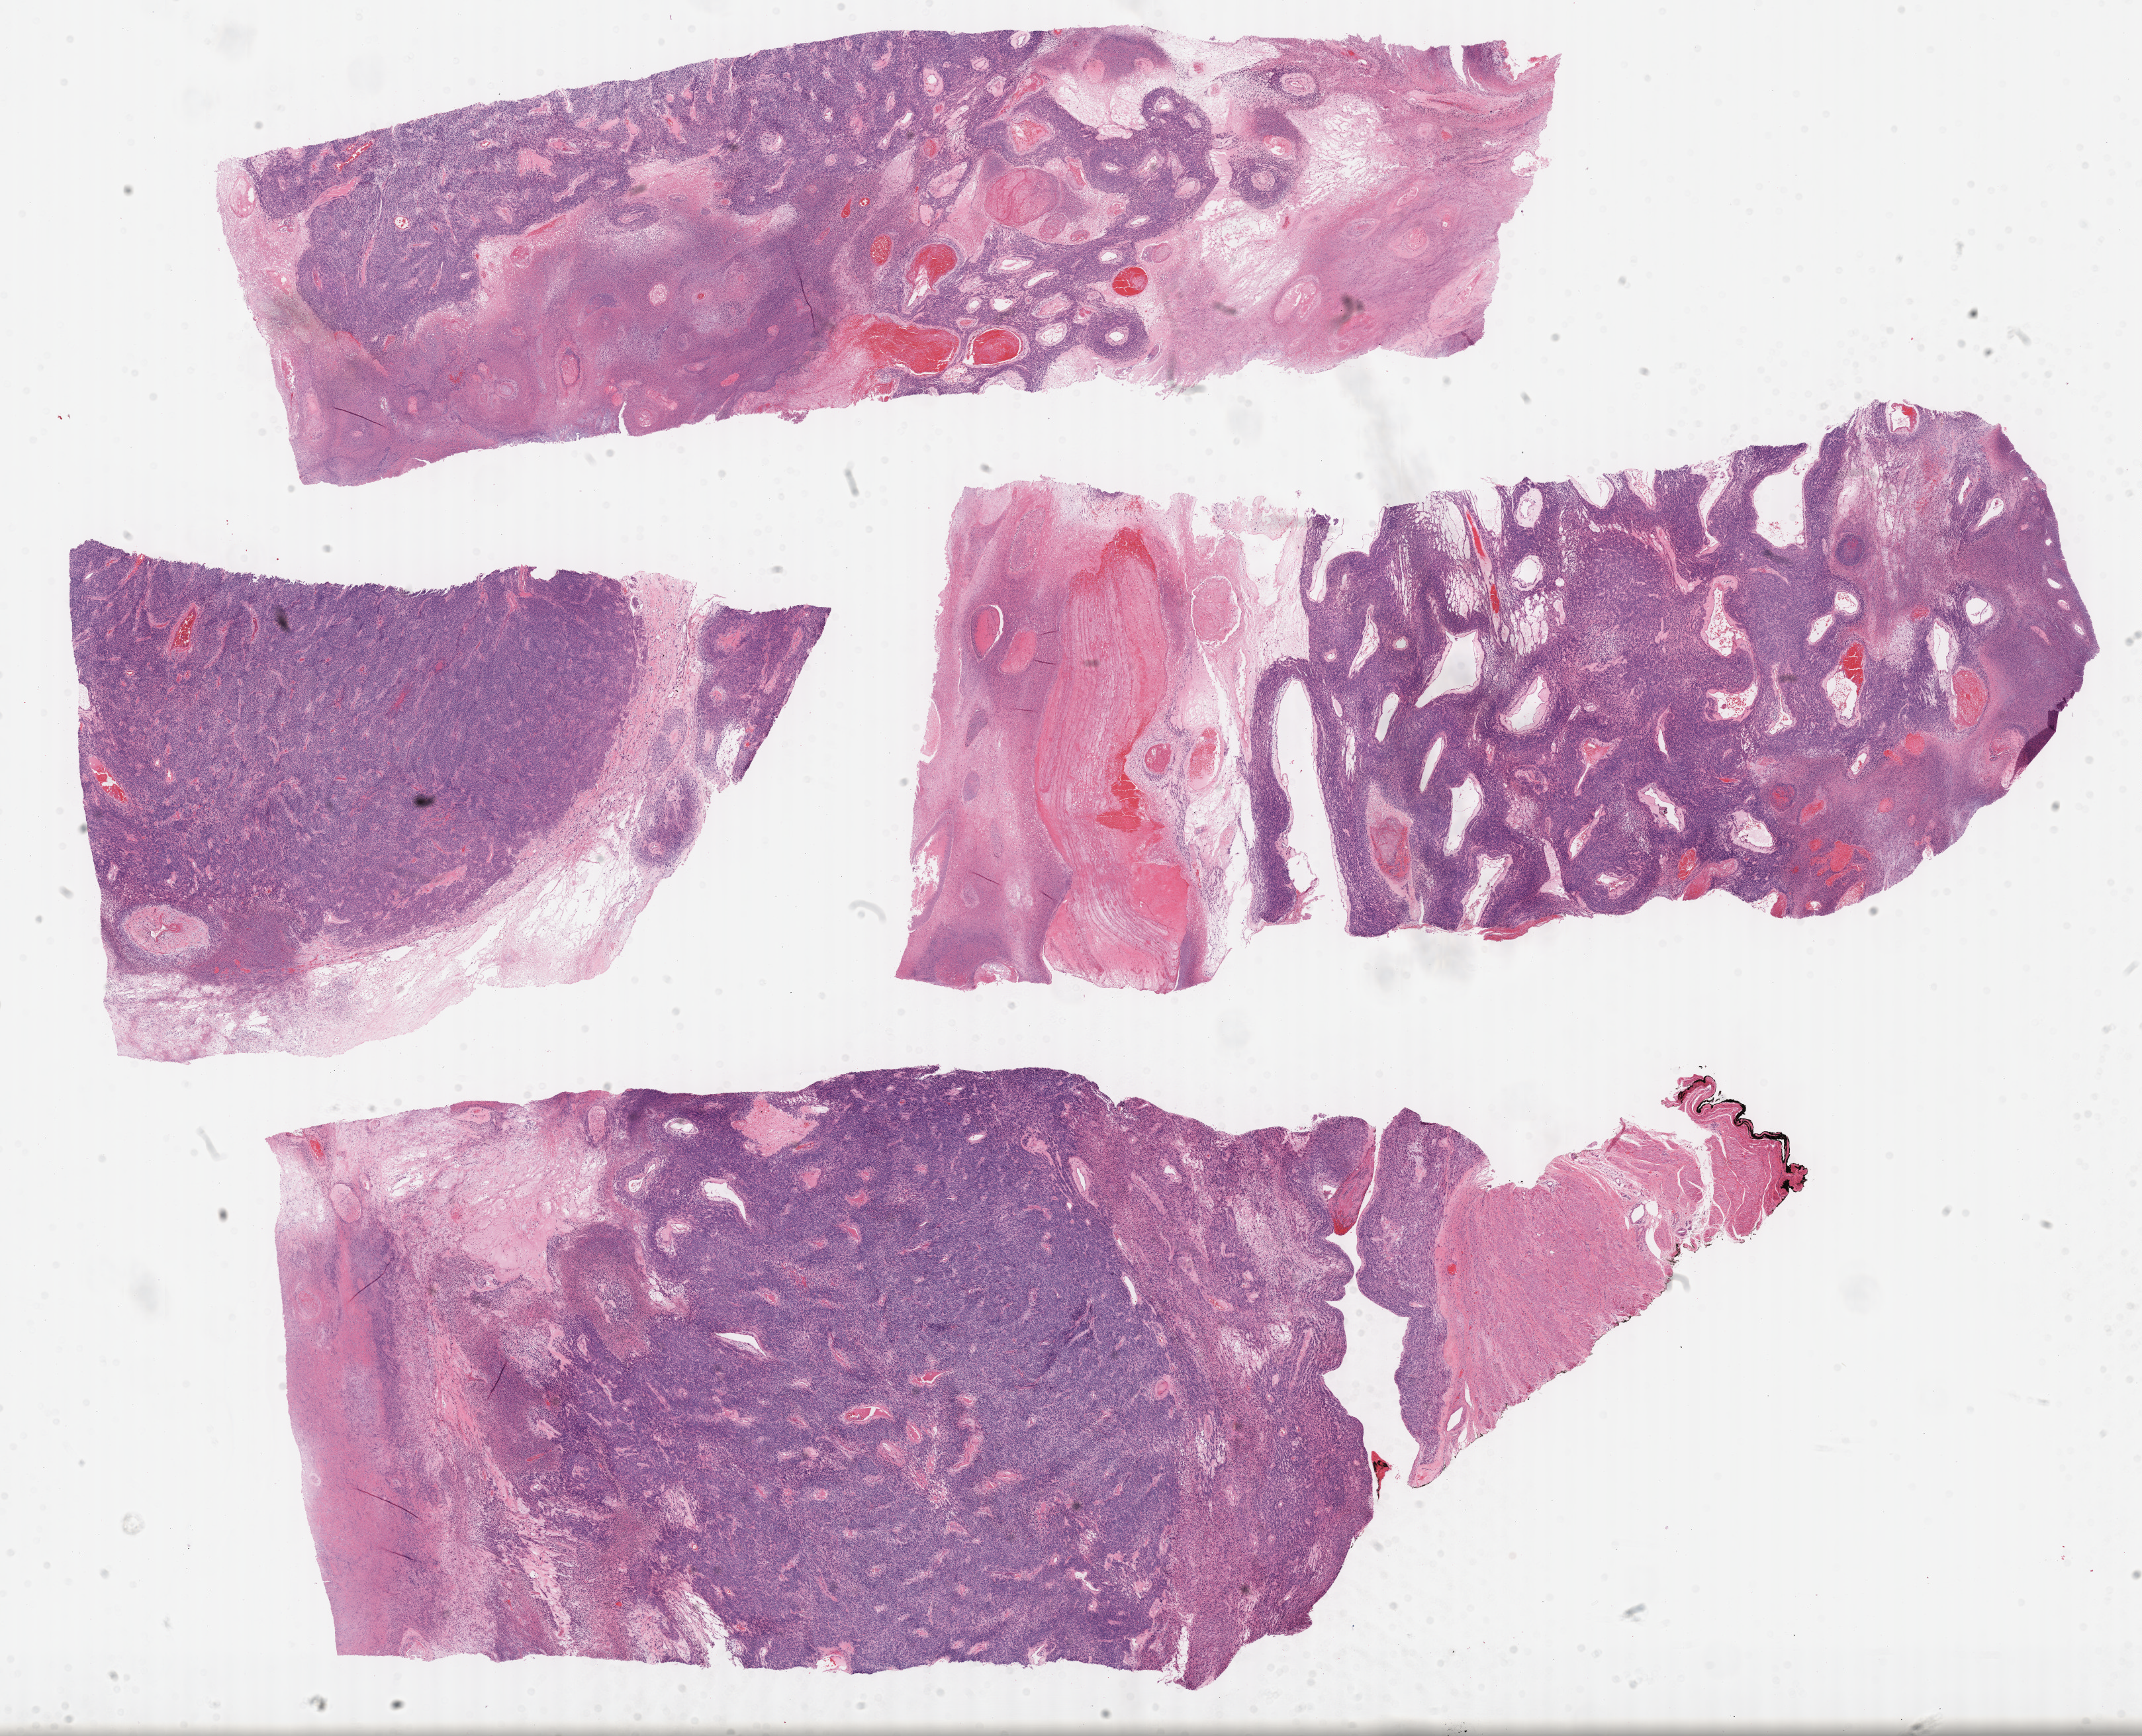
Hematoxylin and eosin (H&E) stained whole-slide image, shown as a low-resolution overview of the whole scanned area (about 26.2 x 21.2 mm); FFPE section; uterus, primary tumour sample. Female patient; age at initial diagnosis 69 years.
Diagnosis: Leiomyosarcoma, NOS.